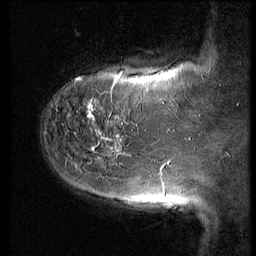
Breast MRI (dynamic contrast-enhanced), one sagittal slice. Position 13 of 64 along the scan axis. 3 images stored at this slice position (order not interpretable as contrast timing). 1.5 T. TE 4.2 ms, TR 9 ms. 2.5 mm slice thickness. 256 × 256 image matrix, field of view 180 × 180 mm. Female patient, age 59 years. From the clinical record (not read from this slice): setting: breast cancer imaged before/during neoadjuvant chemotherapy; receptor status: HER2-positive.
Annotated regions visible in this slice (semi-automatic segmentation, software-assisted and operator-edited):
- analysis volume of interest (the breast-tissue region the enhancement analysis was run in; not a lesion): box from (x=54, y=65) to (x=155, y=132) px
- tumour enhancement mask (voxels above the 140 % enhancement threshold inside the analysis volume of interest): (x=88, y=105)–(x=94, y=118)